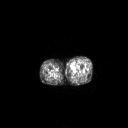
FDG PET of an extremity soft-tissue mass (from a PET/CT study), one axial slice. Position 232 of 267 along the scan axis. 3.27 mm slice thickness. 128 × 128 image matrix, field of view 700 × 700 mm. Patient: male, 48 years. From the clinical record (not read from this slice): histological type: pleiomorphic leiomyosarcoma; grade: high; site of the primary tumour: left thigh.
Annotated regions visible in this slice (expert contour drawn on MRI and transferred to this co-registered scan by the dataset authors):
- gross tumour volume including surrounding oedema: bounding box <70,64,75,70> (left, top, right, bottom; pixels)